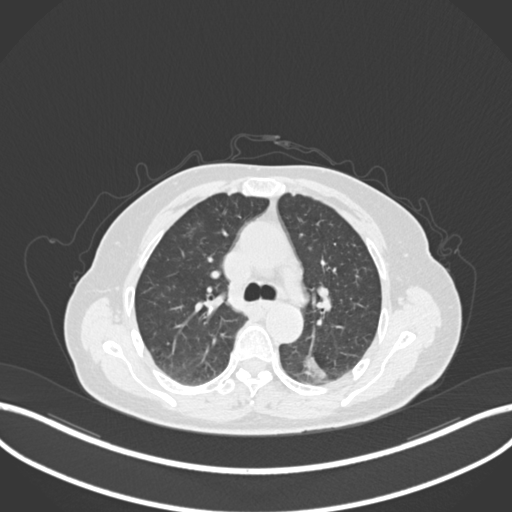
Chest CT, one axial slice. Slice 544 of 727 in the series (ordered by position). Reconstruction kernel B30f. 120 kVp. Lung window (W 1500 / L -600 HU). 1 mm slice thickness. 512 × 512 image matrix, field of view 400 × 400 mm. Female patient, age 70 years. From the clinical record (not read from this slice): clinical TNM (as recorded): T1c N0 M0.
Structures marked on this image (rectangle marked by the reading radiologist):
- lung tumour (recorded histology: adenocarcinoma): box from (x=298, y=351) to (x=334, y=387) px